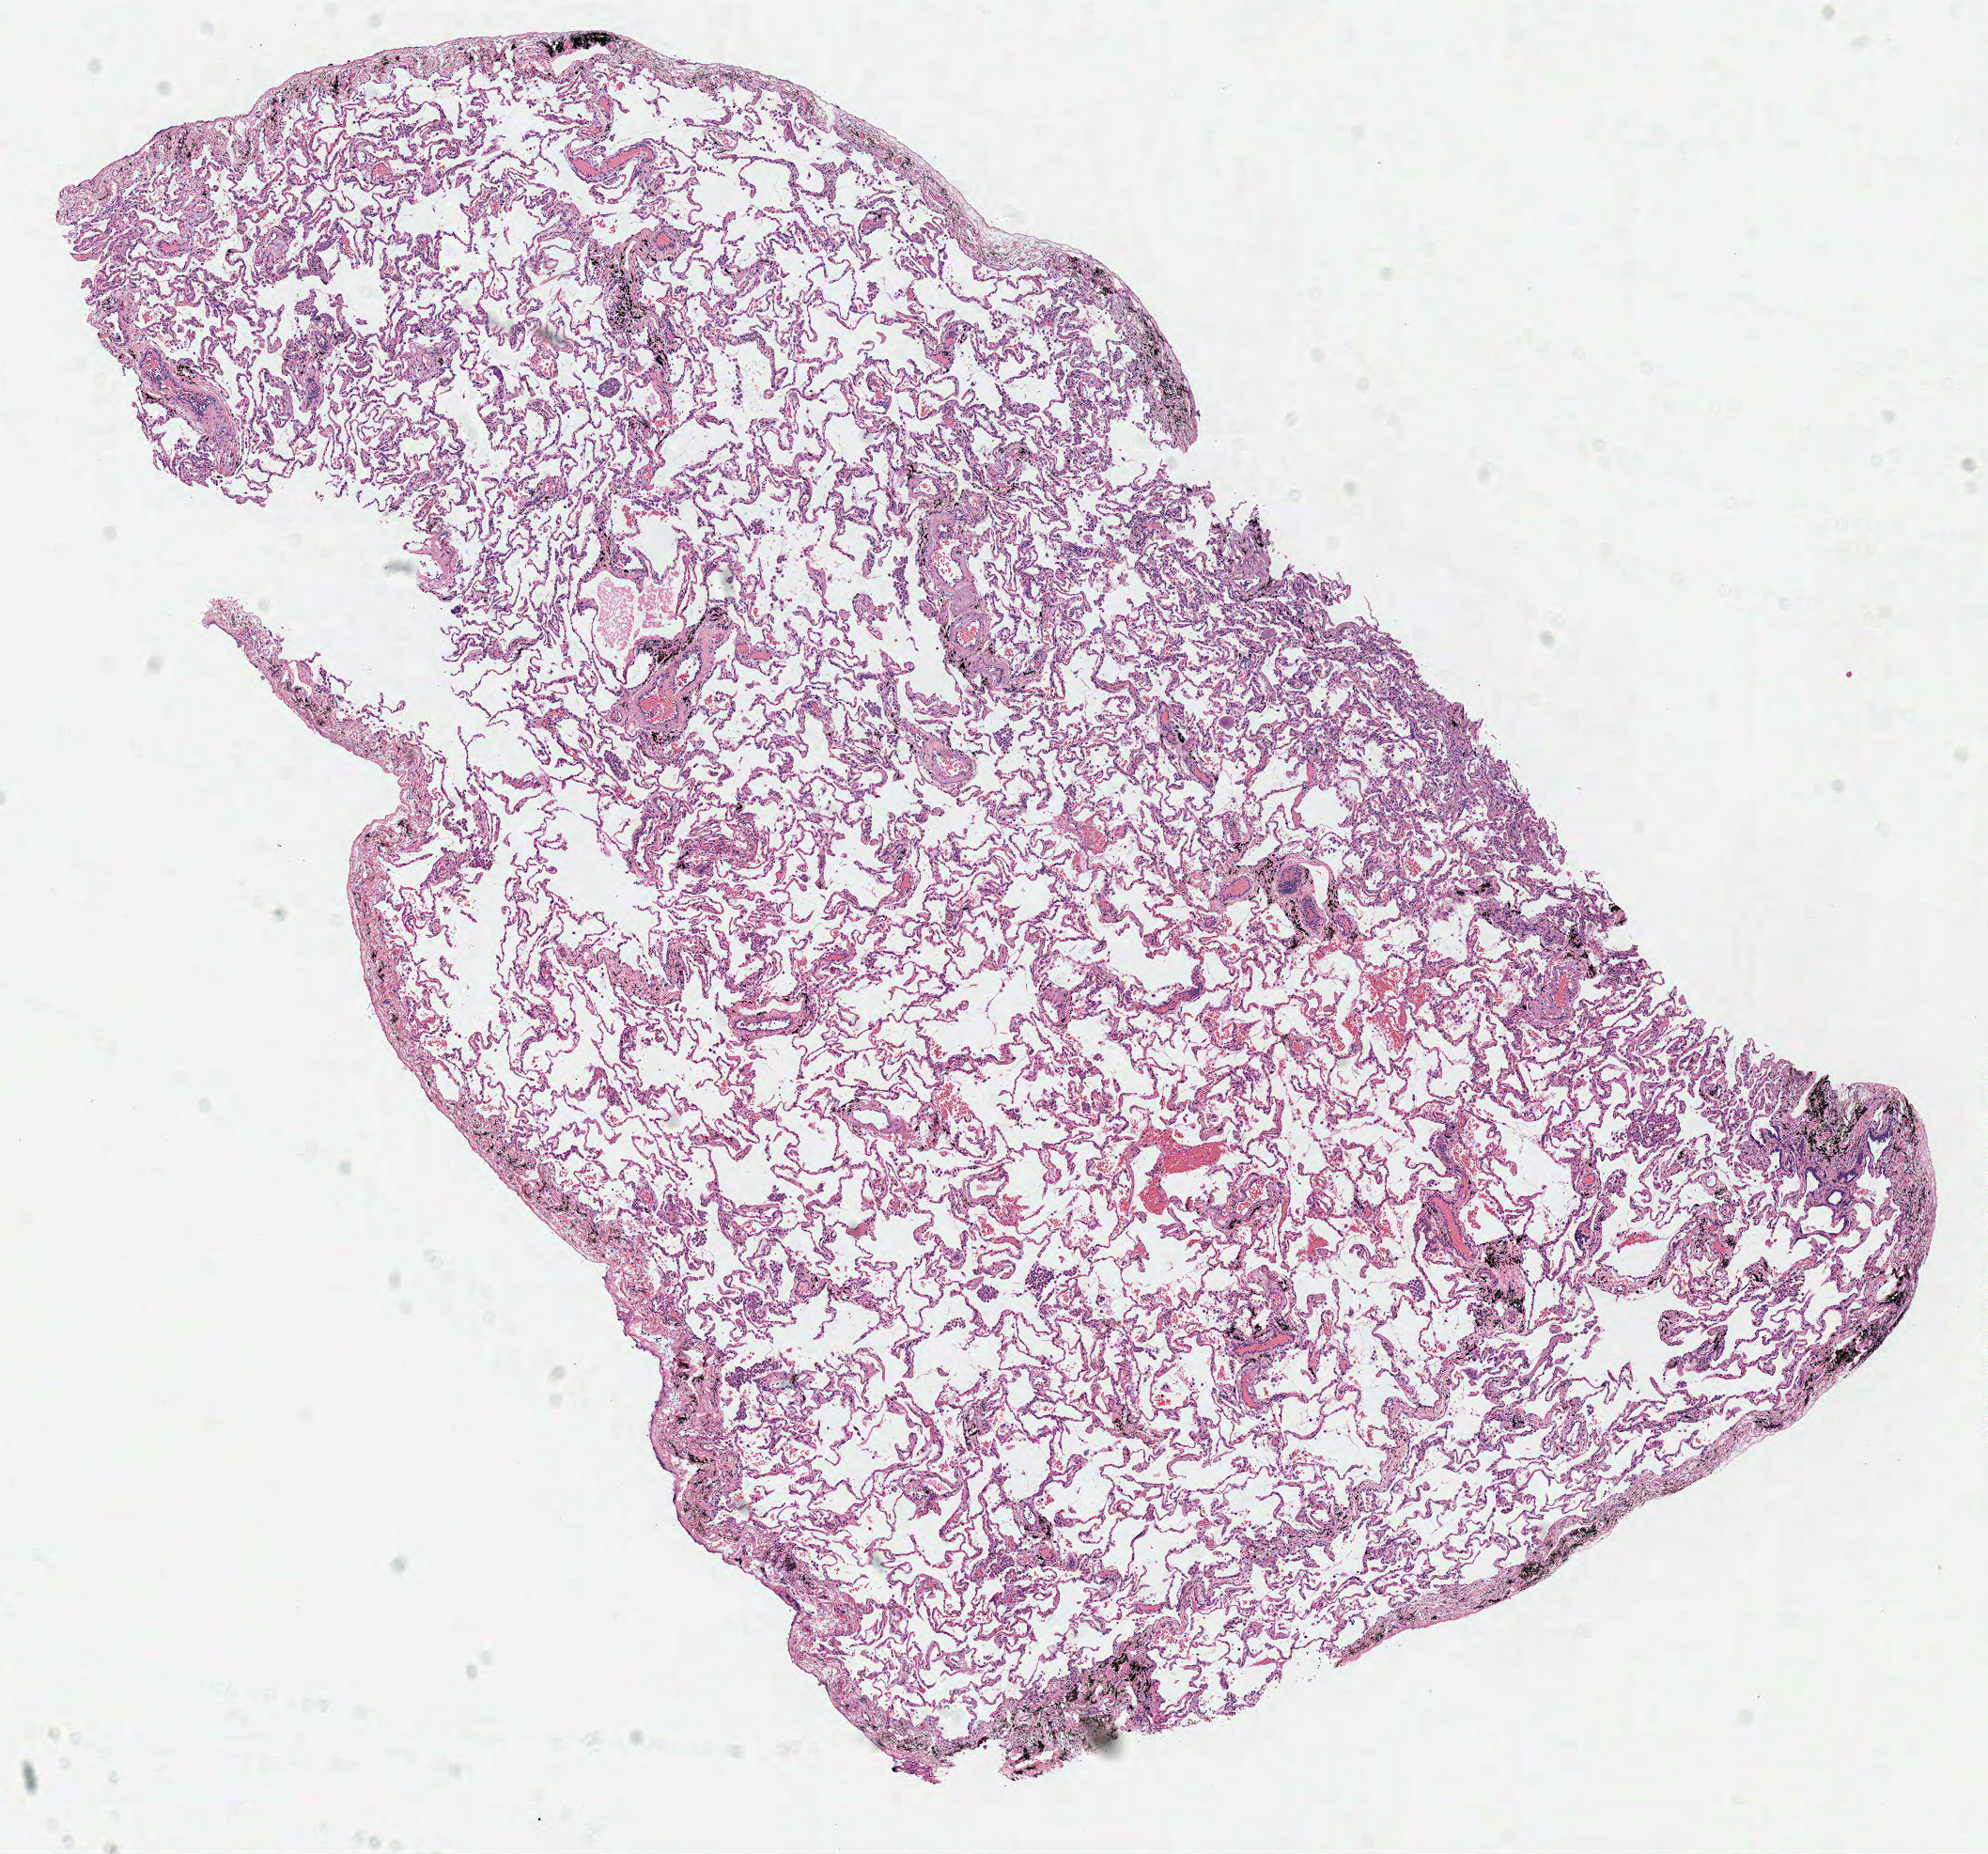
Hematoxylin and eosin (H&E) stained whole-slide image — whole scanned area (about 8.3 x 7.8 mm, from a 40x scan) shown as a low-resolution overview; frozen section from the top of the tissue portion; sample: solid tissue normal (non-tumour tissue), lung. Patient: male, age at initial diagnosis 85 years.
- this section: solid tissue normal (non-tumour) sample from the same patient
- patient diagnosis: Squamous cell carcinoma, NOS (upper lobe, lung)